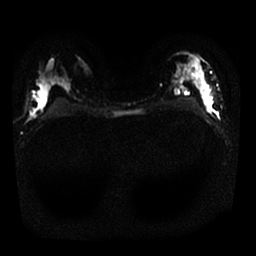
Breast MRI, one axial slice. Slice 14 of 25 in the series (ordered by position). Diffusion-weighted series; image 2 of 4 stored at this slice position (different b-values; order by instance number). 1.5 T. 256 × 256 image matrix, field of view 320 × 320 mm. Female patient.
Annotated regions visible in this slice (expert manual segmentation):
- tumour on diffusion-weighted imaging: bounding box (x1, y1, x2, y2) in pixels: (196, 70, 212, 106)